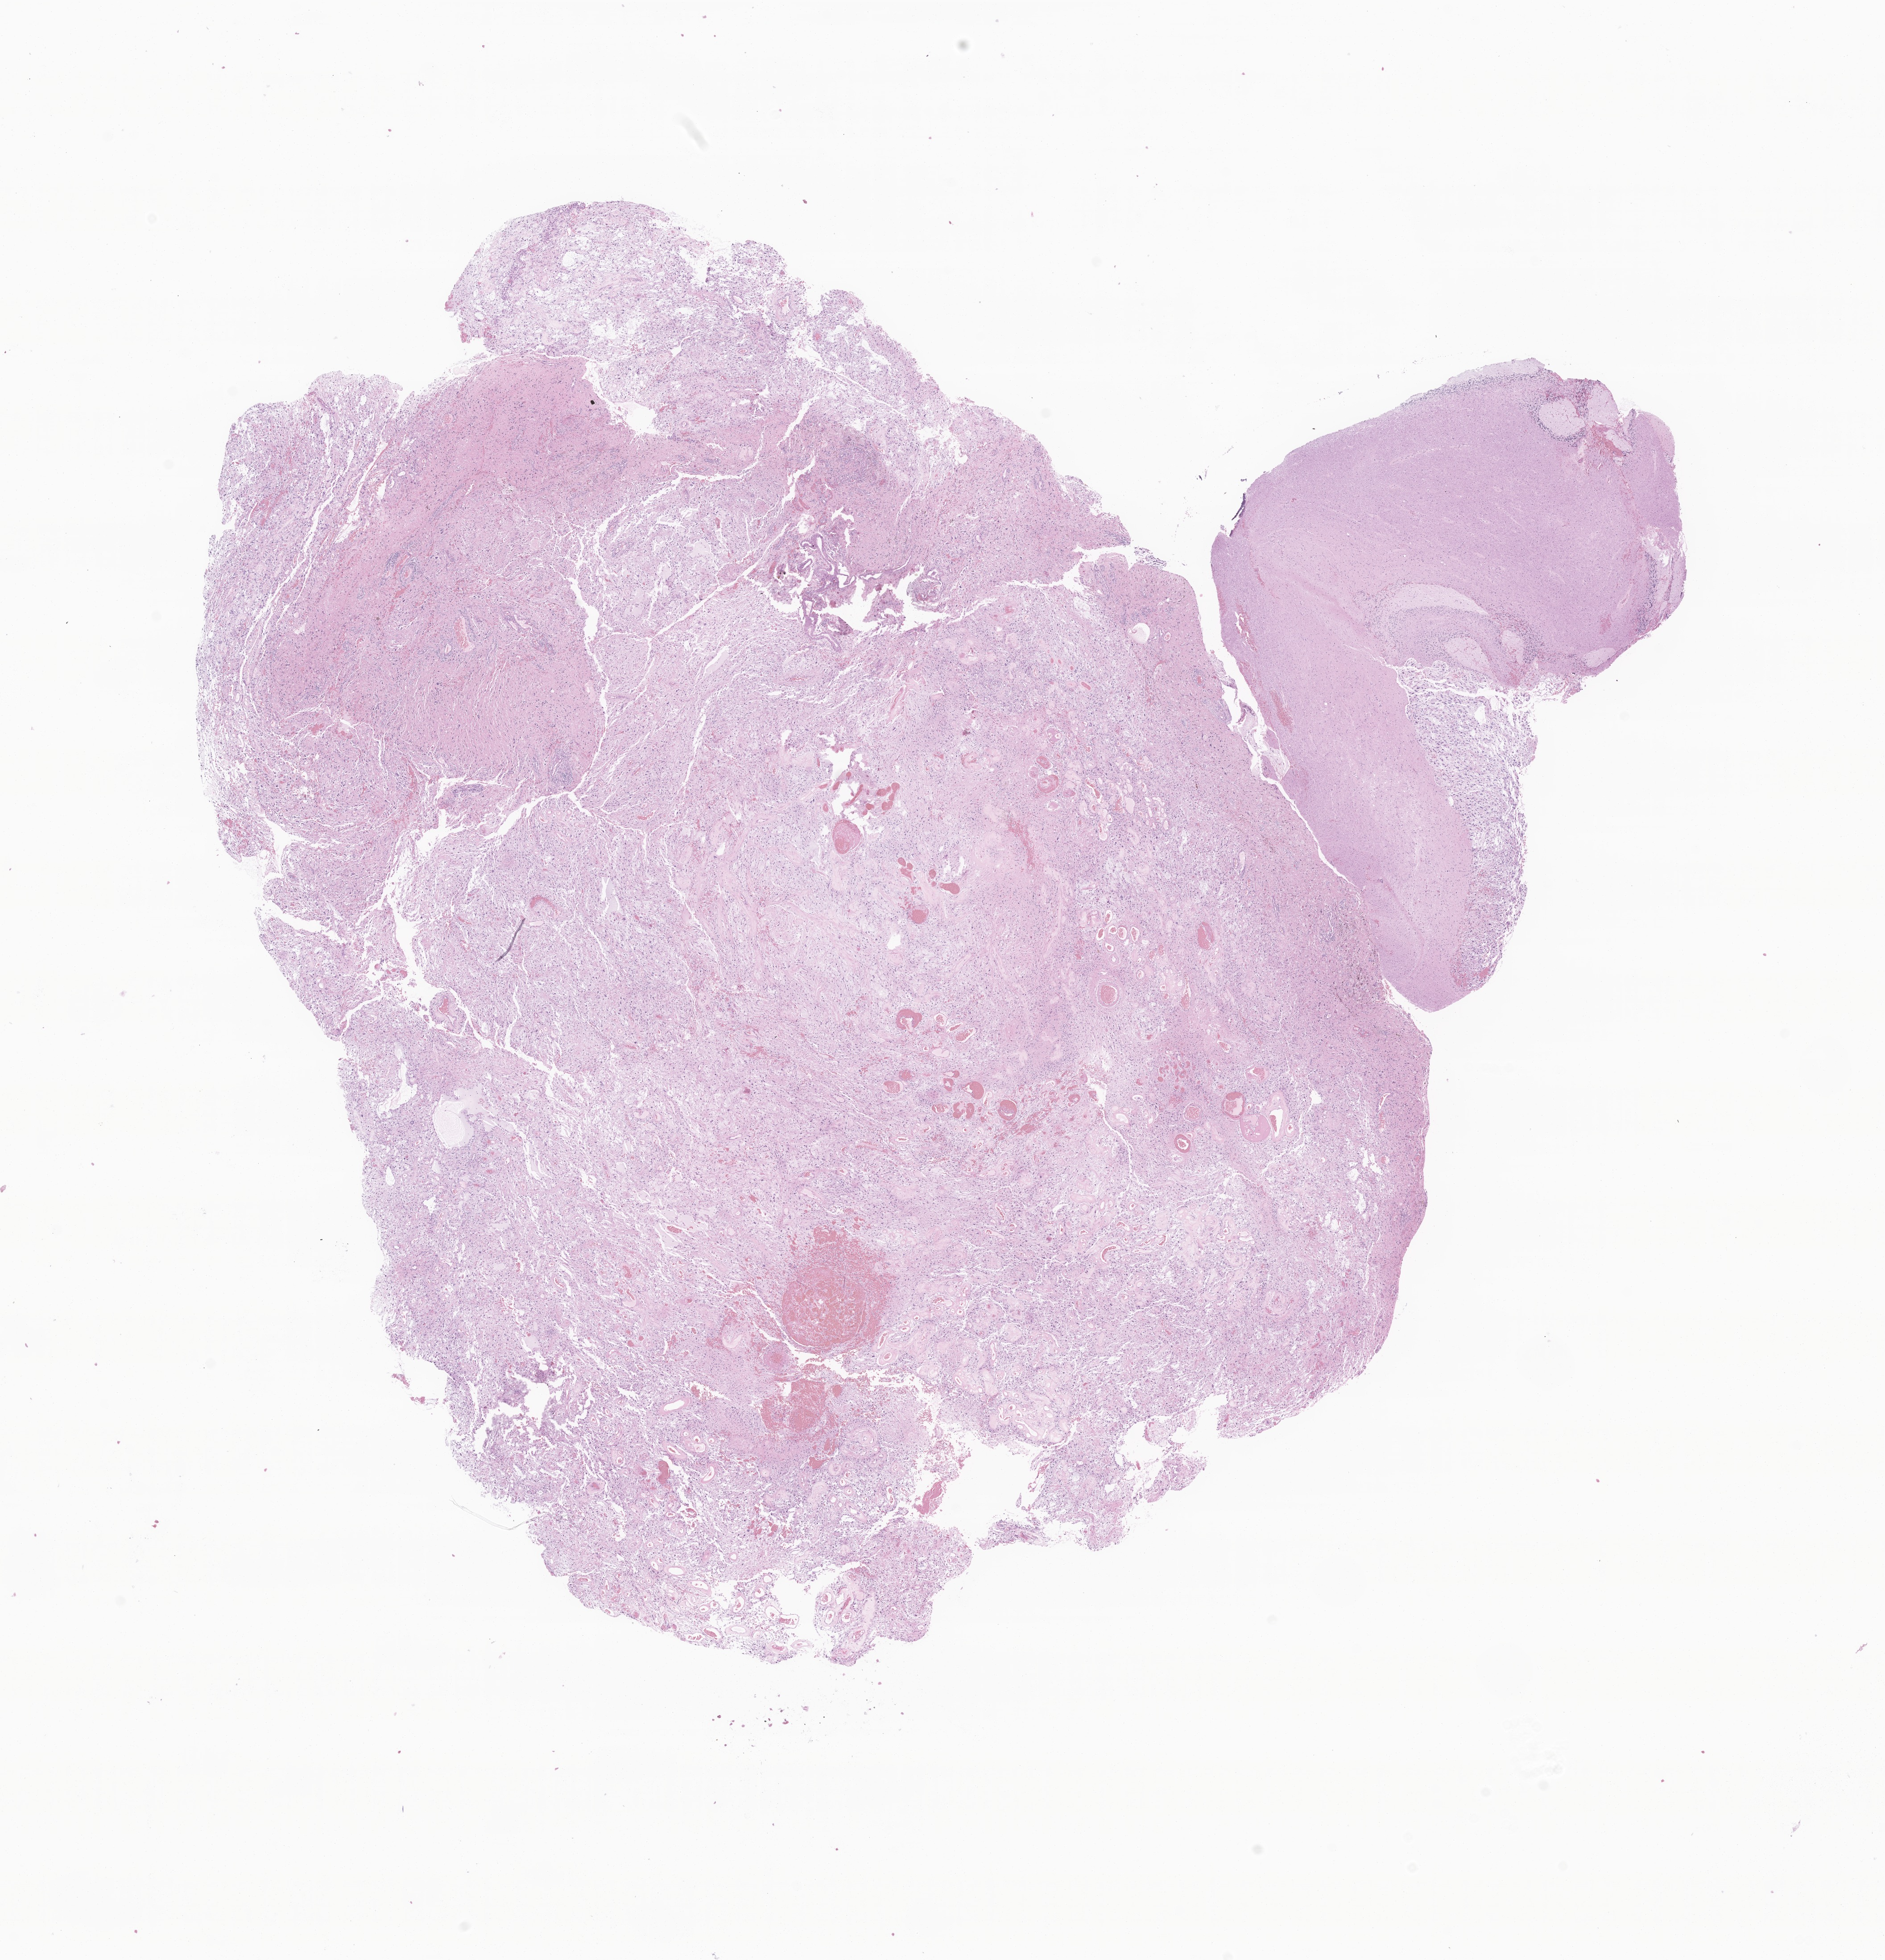
Digitized H&E-stained section of tumor tissue from the brain — shown as a low-resolution overview of the whole scanned area (about 17.8 x 18.5 mm), formalin-fixed paraffin-embedded section. Patient female; age 209 months (17 years 5 months).
• diagnosis (ICD-O-3 morphology term): Pilocytic astrocytoma